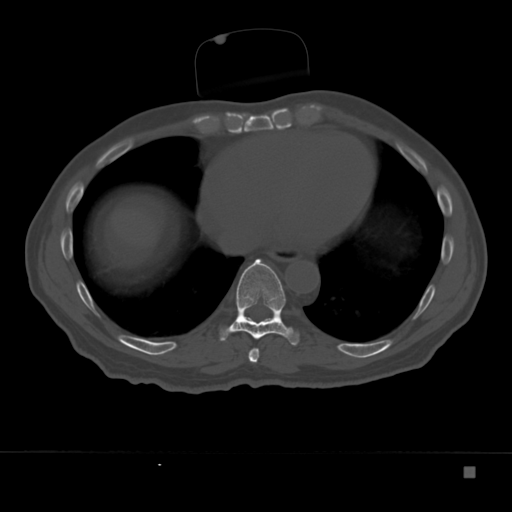
CT including the spine, one axial slice; slice 190 of 332 in the series (ordered by position); 120 kVp; bone window (W 1800 / L 400 HU); 1.5 mm slice thickness; 512 × 512 image matrix, field of view 389 × 389 mm. Patient: male, 72 years. Case-level facts recorded for this patient, not image findings: primary cancer: skeletal.
Annotated regions visible in this slice (semi-automatic segmentation, software-assisted and operator-edited):
- T8 vertebra: bounding box (x1, y1, x2, y2) in pixels: (248, 348, 260, 363)
- T9 vertebra: (220, 259, 299, 346)